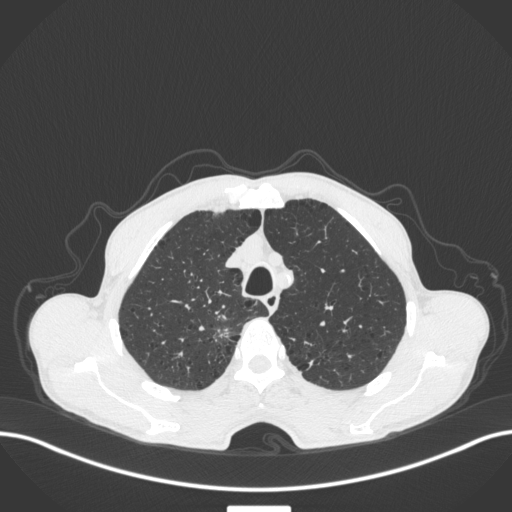
Chest CT, one axial slice. Reconstruction kernel B31f. Lung window (W 1500 / L -600 HU). 1 mm slice thickness. 512 × 512 image matrix, field of view 400 × 400 mm. Male patient, age 70 years. Case-level facts recorded for this patient, not image findings: clinical TNM (as recorded): T1a N0 M0.
Structures marked on this image (rectangle marked by the reading radiologist):
- lung tumour (recorded histology: adenocarcinoma): bounding box (x1, y1, x2, y2) in pixels: (208, 314, 239, 345)